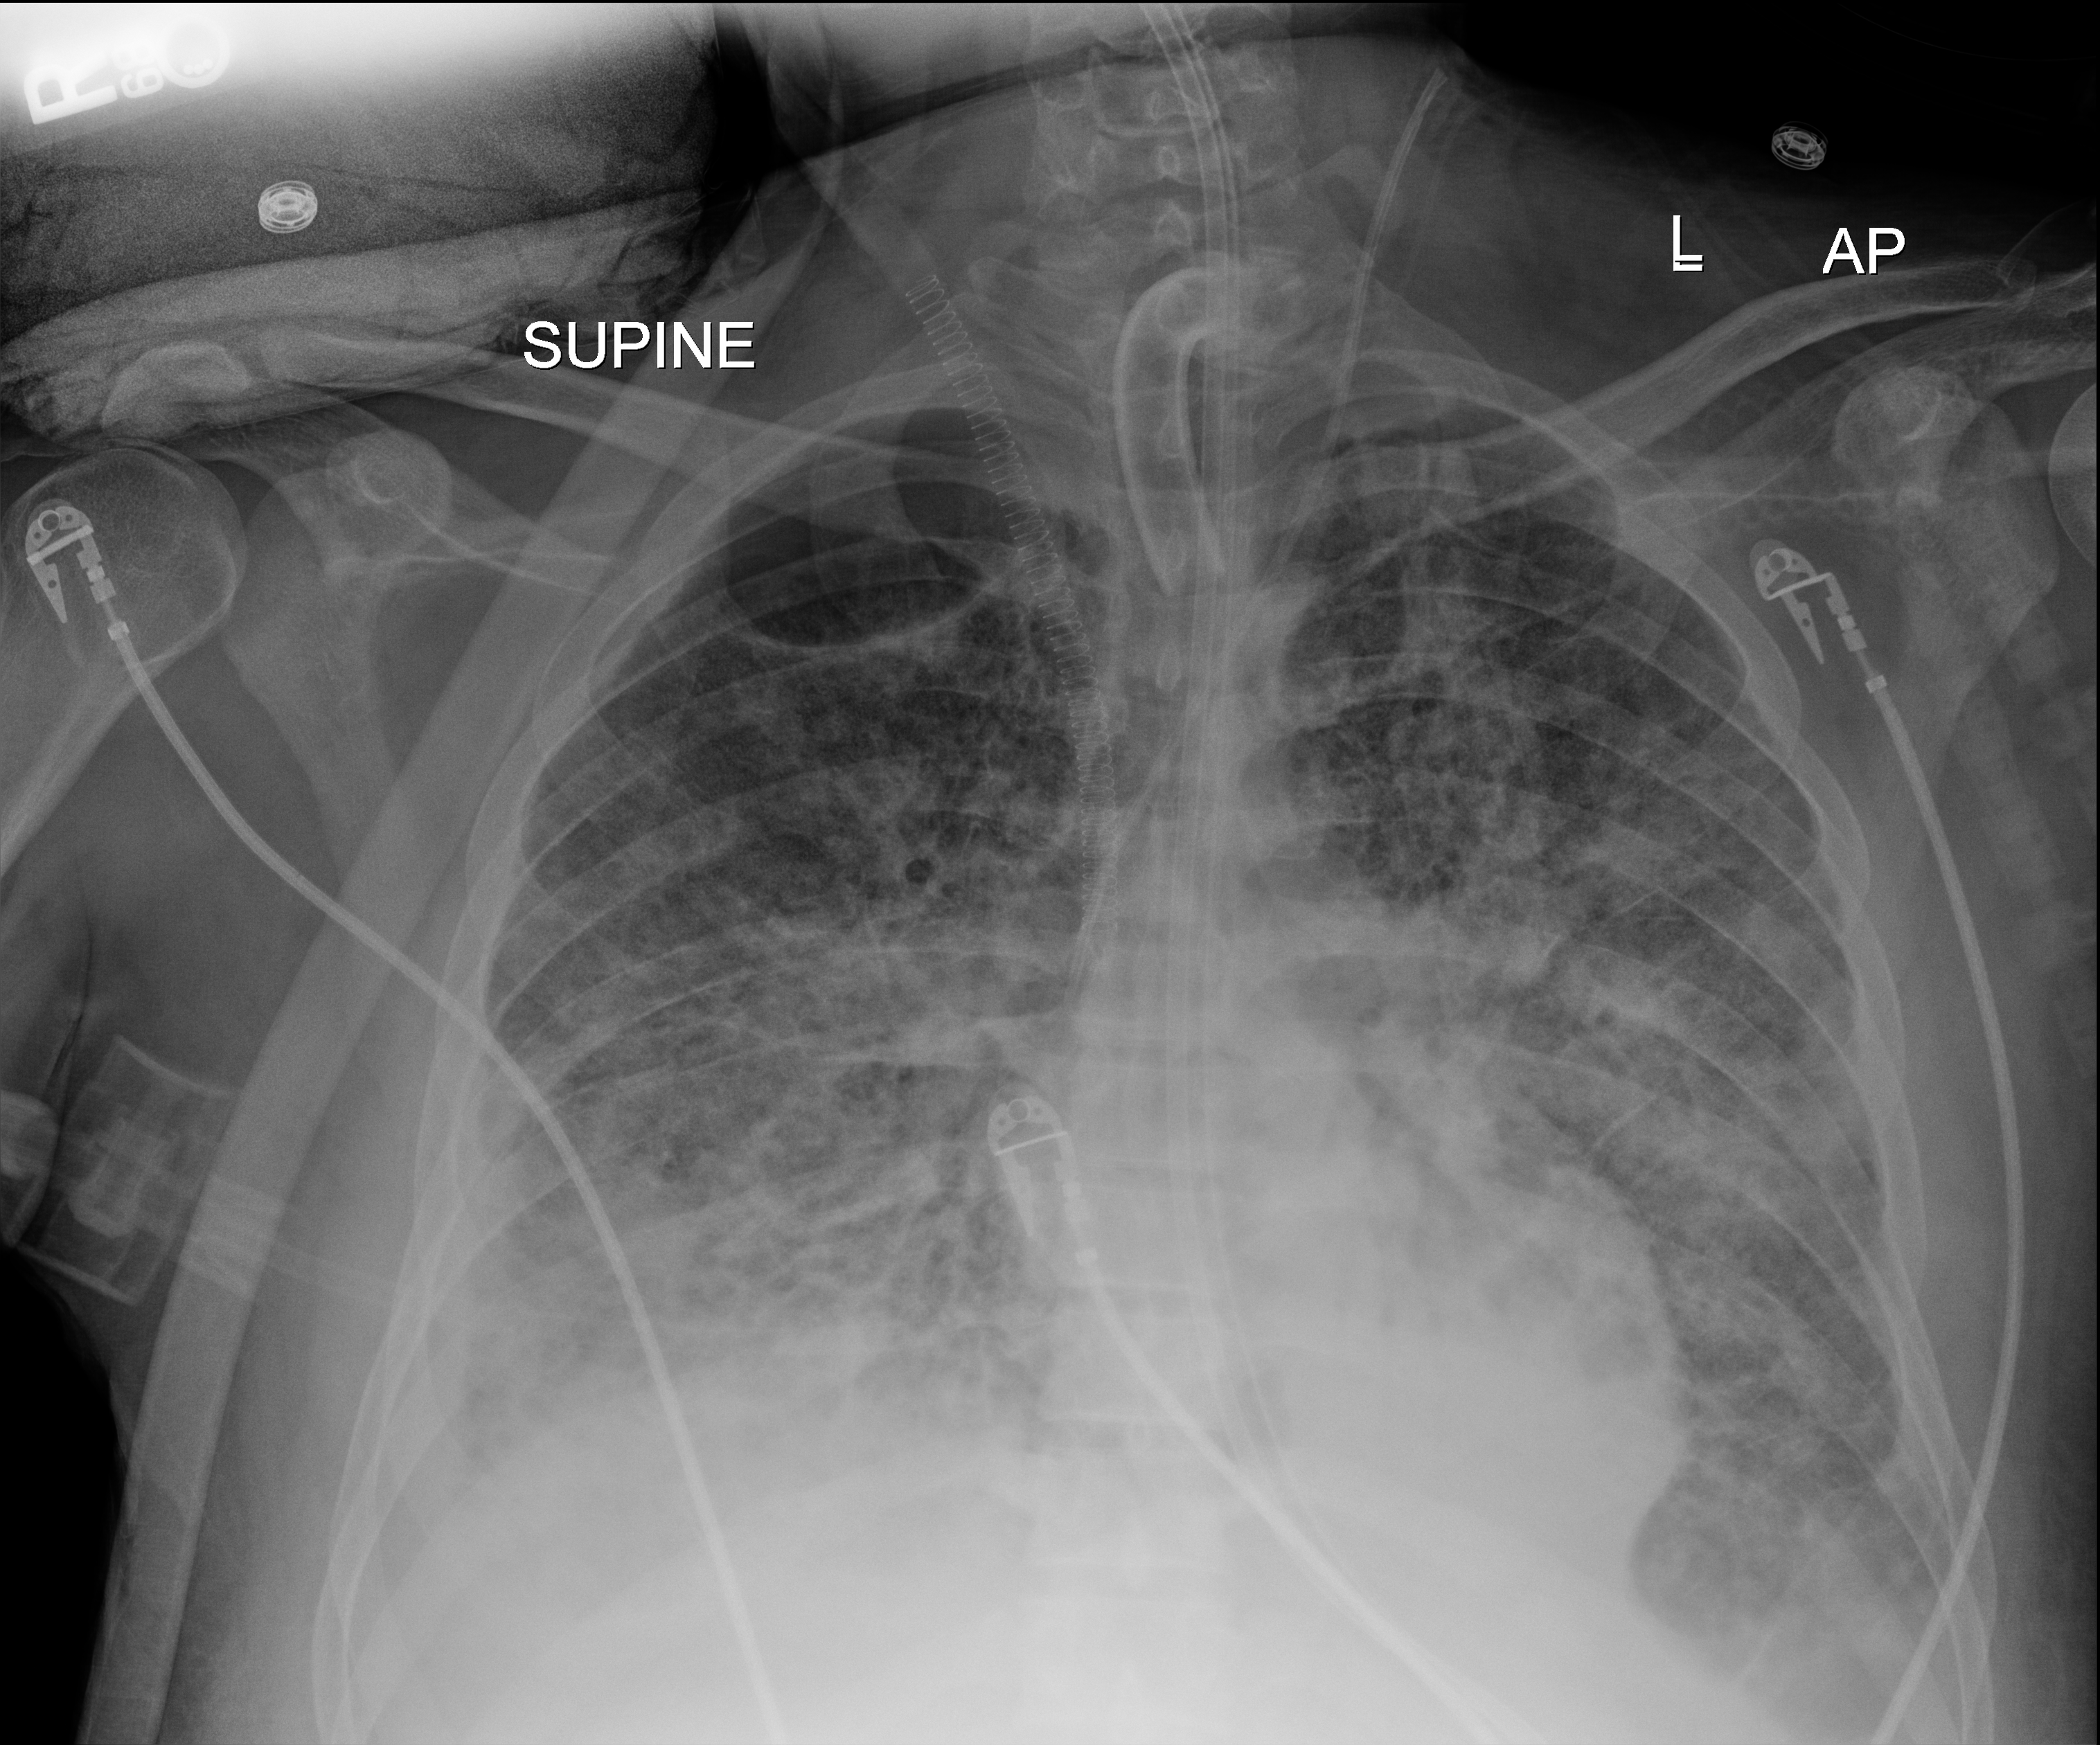
Chest radiograph (digital radiography). Adult patient hospitalised with COVID-19, age 18–59 years.
From the hospital-stay record, not from the radiograph (when in the stay this image was taken is not recorded): smoking status (admission record): never; hypertension (admission record): no; mechanically ventilated during this hospital stay: yes.